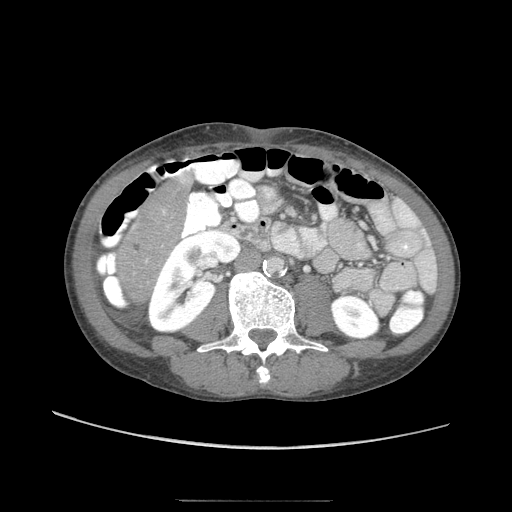
Contrast-enhanced abdominal CT (liver protocol), one axial slice; slice 10 of 103 in the series (ordered by position); reconstruction kernel STANDARD; soft-tissue window (W 400 / L 40 HU); 512 × 512 image matrix, field of view 380 × 380 mm. Case-level facts recorded for this patient, not image findings: diagnosis: hepatocellular carcinoma (patient treated with transarterial chemoembolisation; whether this scan precedes or follows treatment is not stated here); TNM stage (as recorded): Stage-IIIA; Child-Pugh class: A.
Annotated regions visible in this slice (semi-automatic segmentation, software-assisted and operator-edited):
- liver parenchyma outside the tumour (the mass and vessels are separate outlines, so this box may not span the whole liver): bounding box <115,172,193,306> (left, top, right, bottom; pixels)